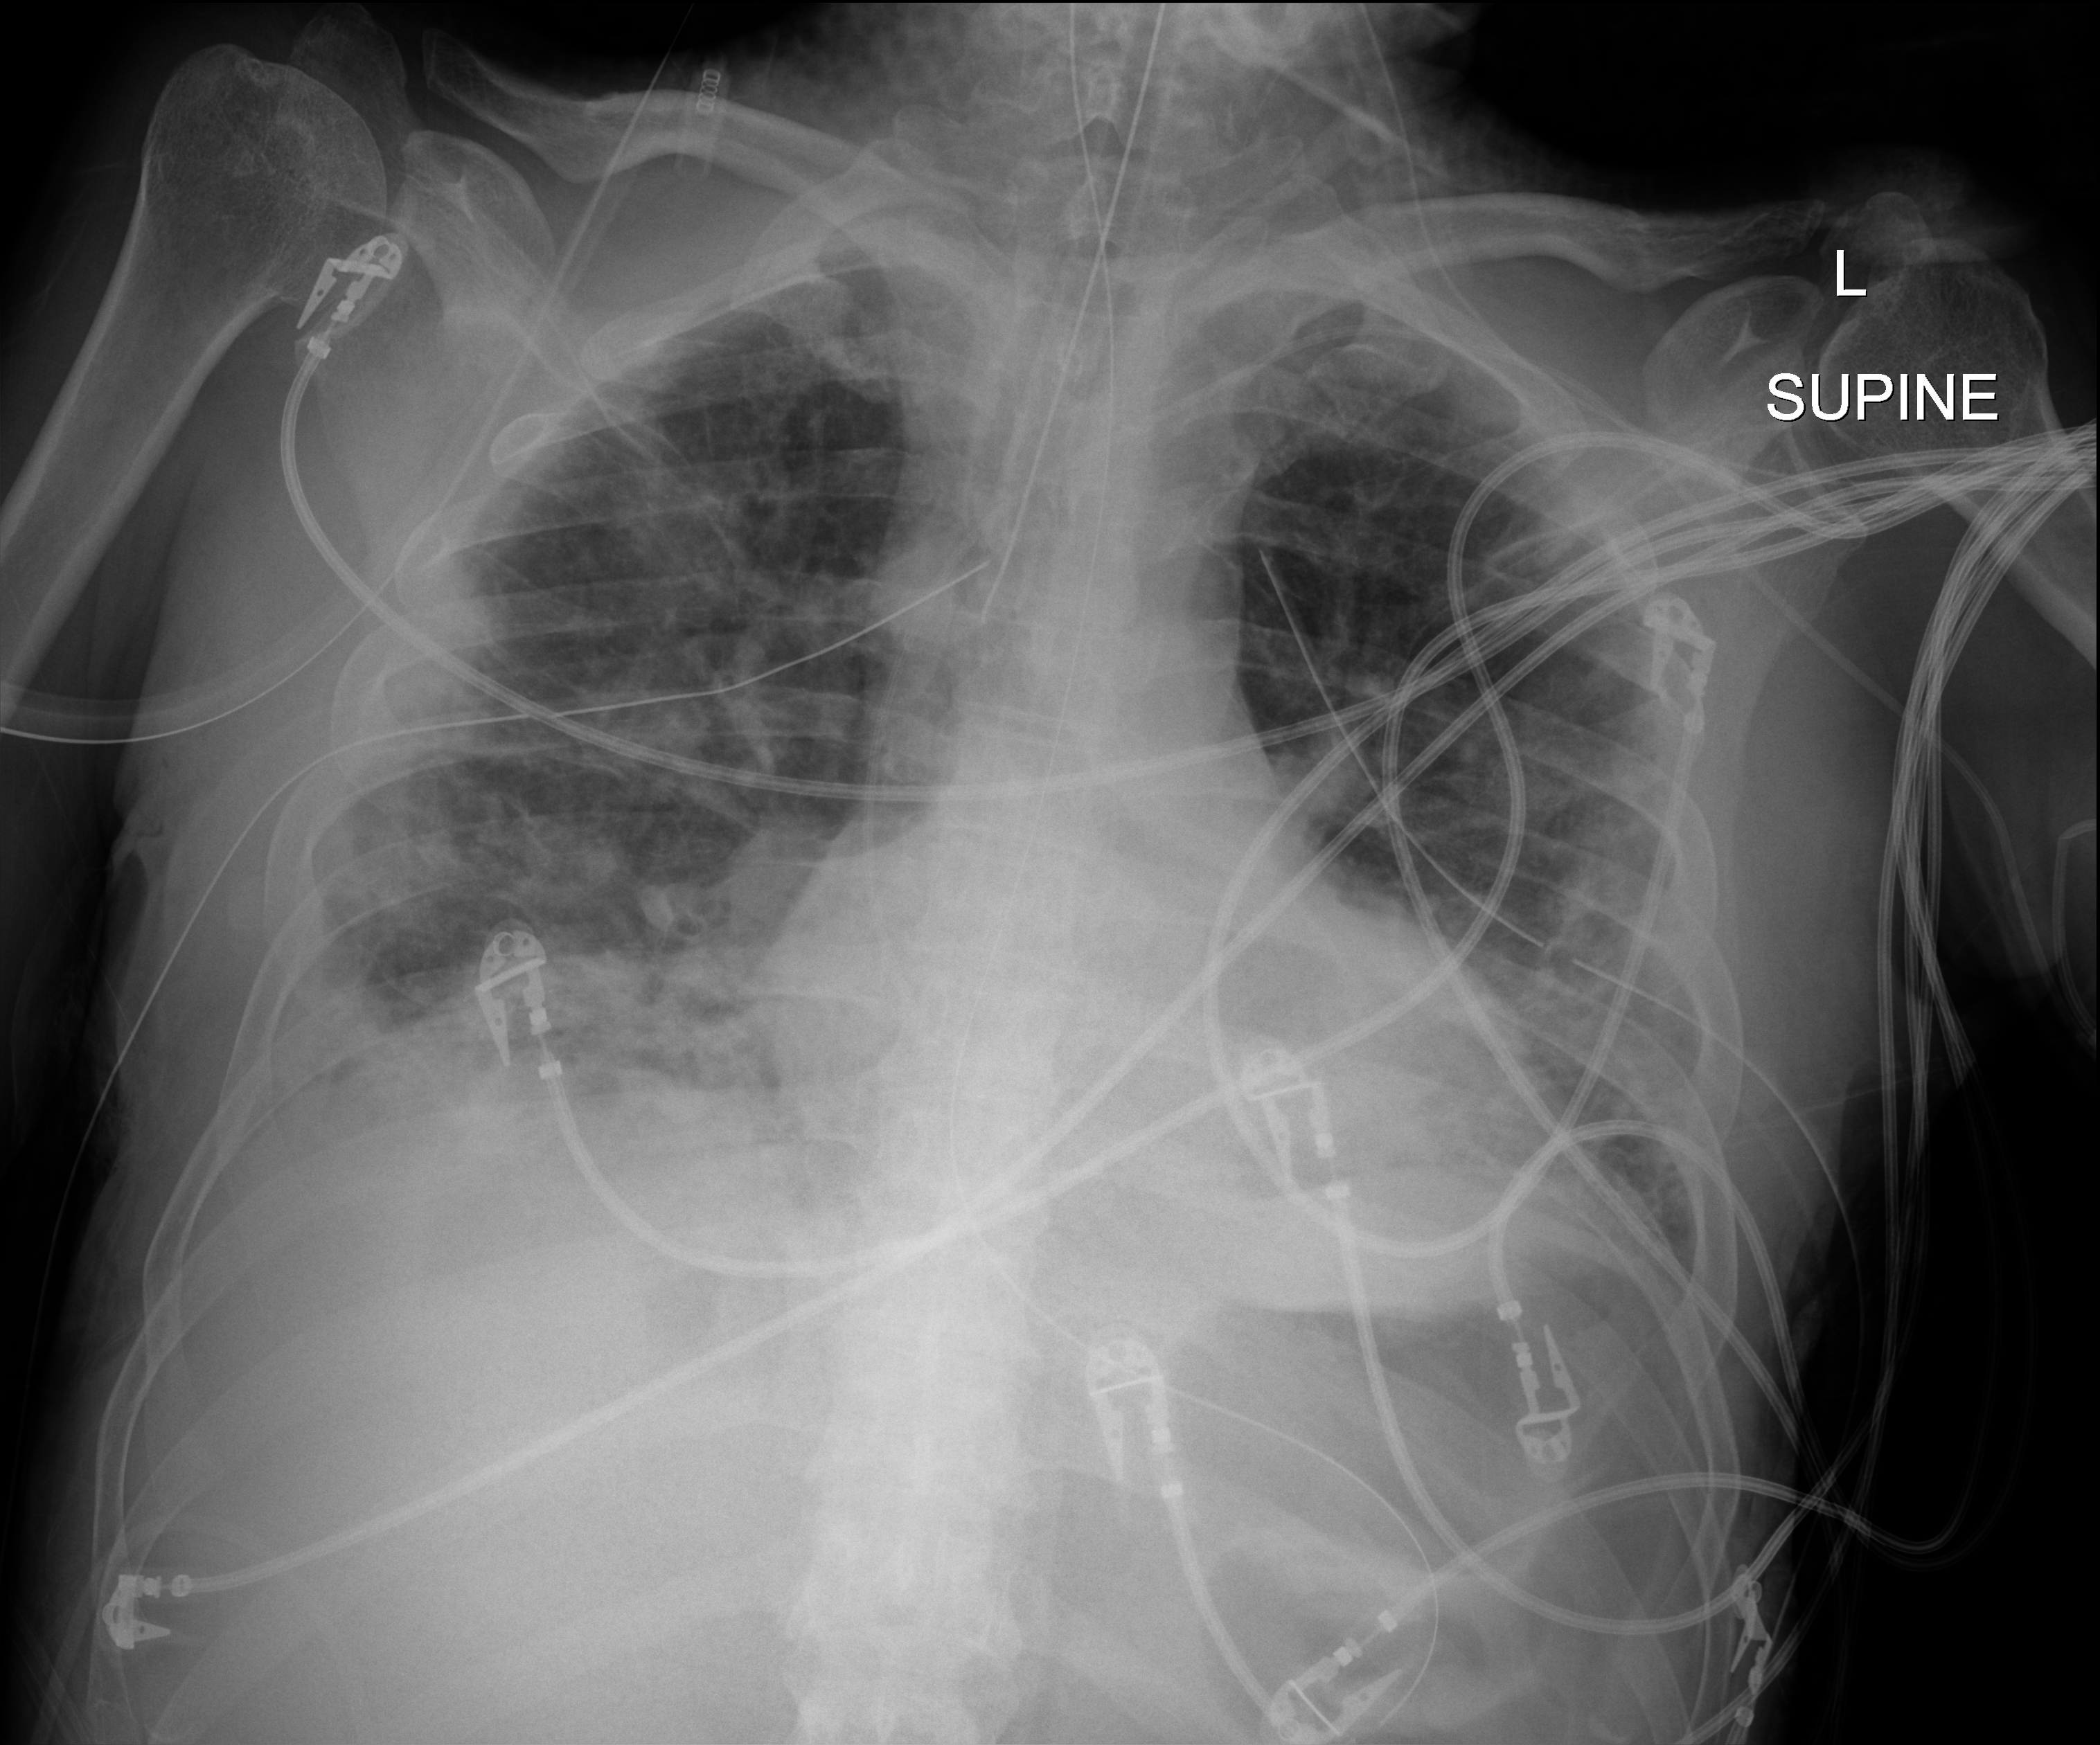
Bedside chest radiograph (digital radiography). Patient hospitalised with COVID-19; male, aged 18–59 years.
From the hospital-stay record, not from the radiograph (when in the stay this image was taken is not recorded): diabetes (admission record): yes.